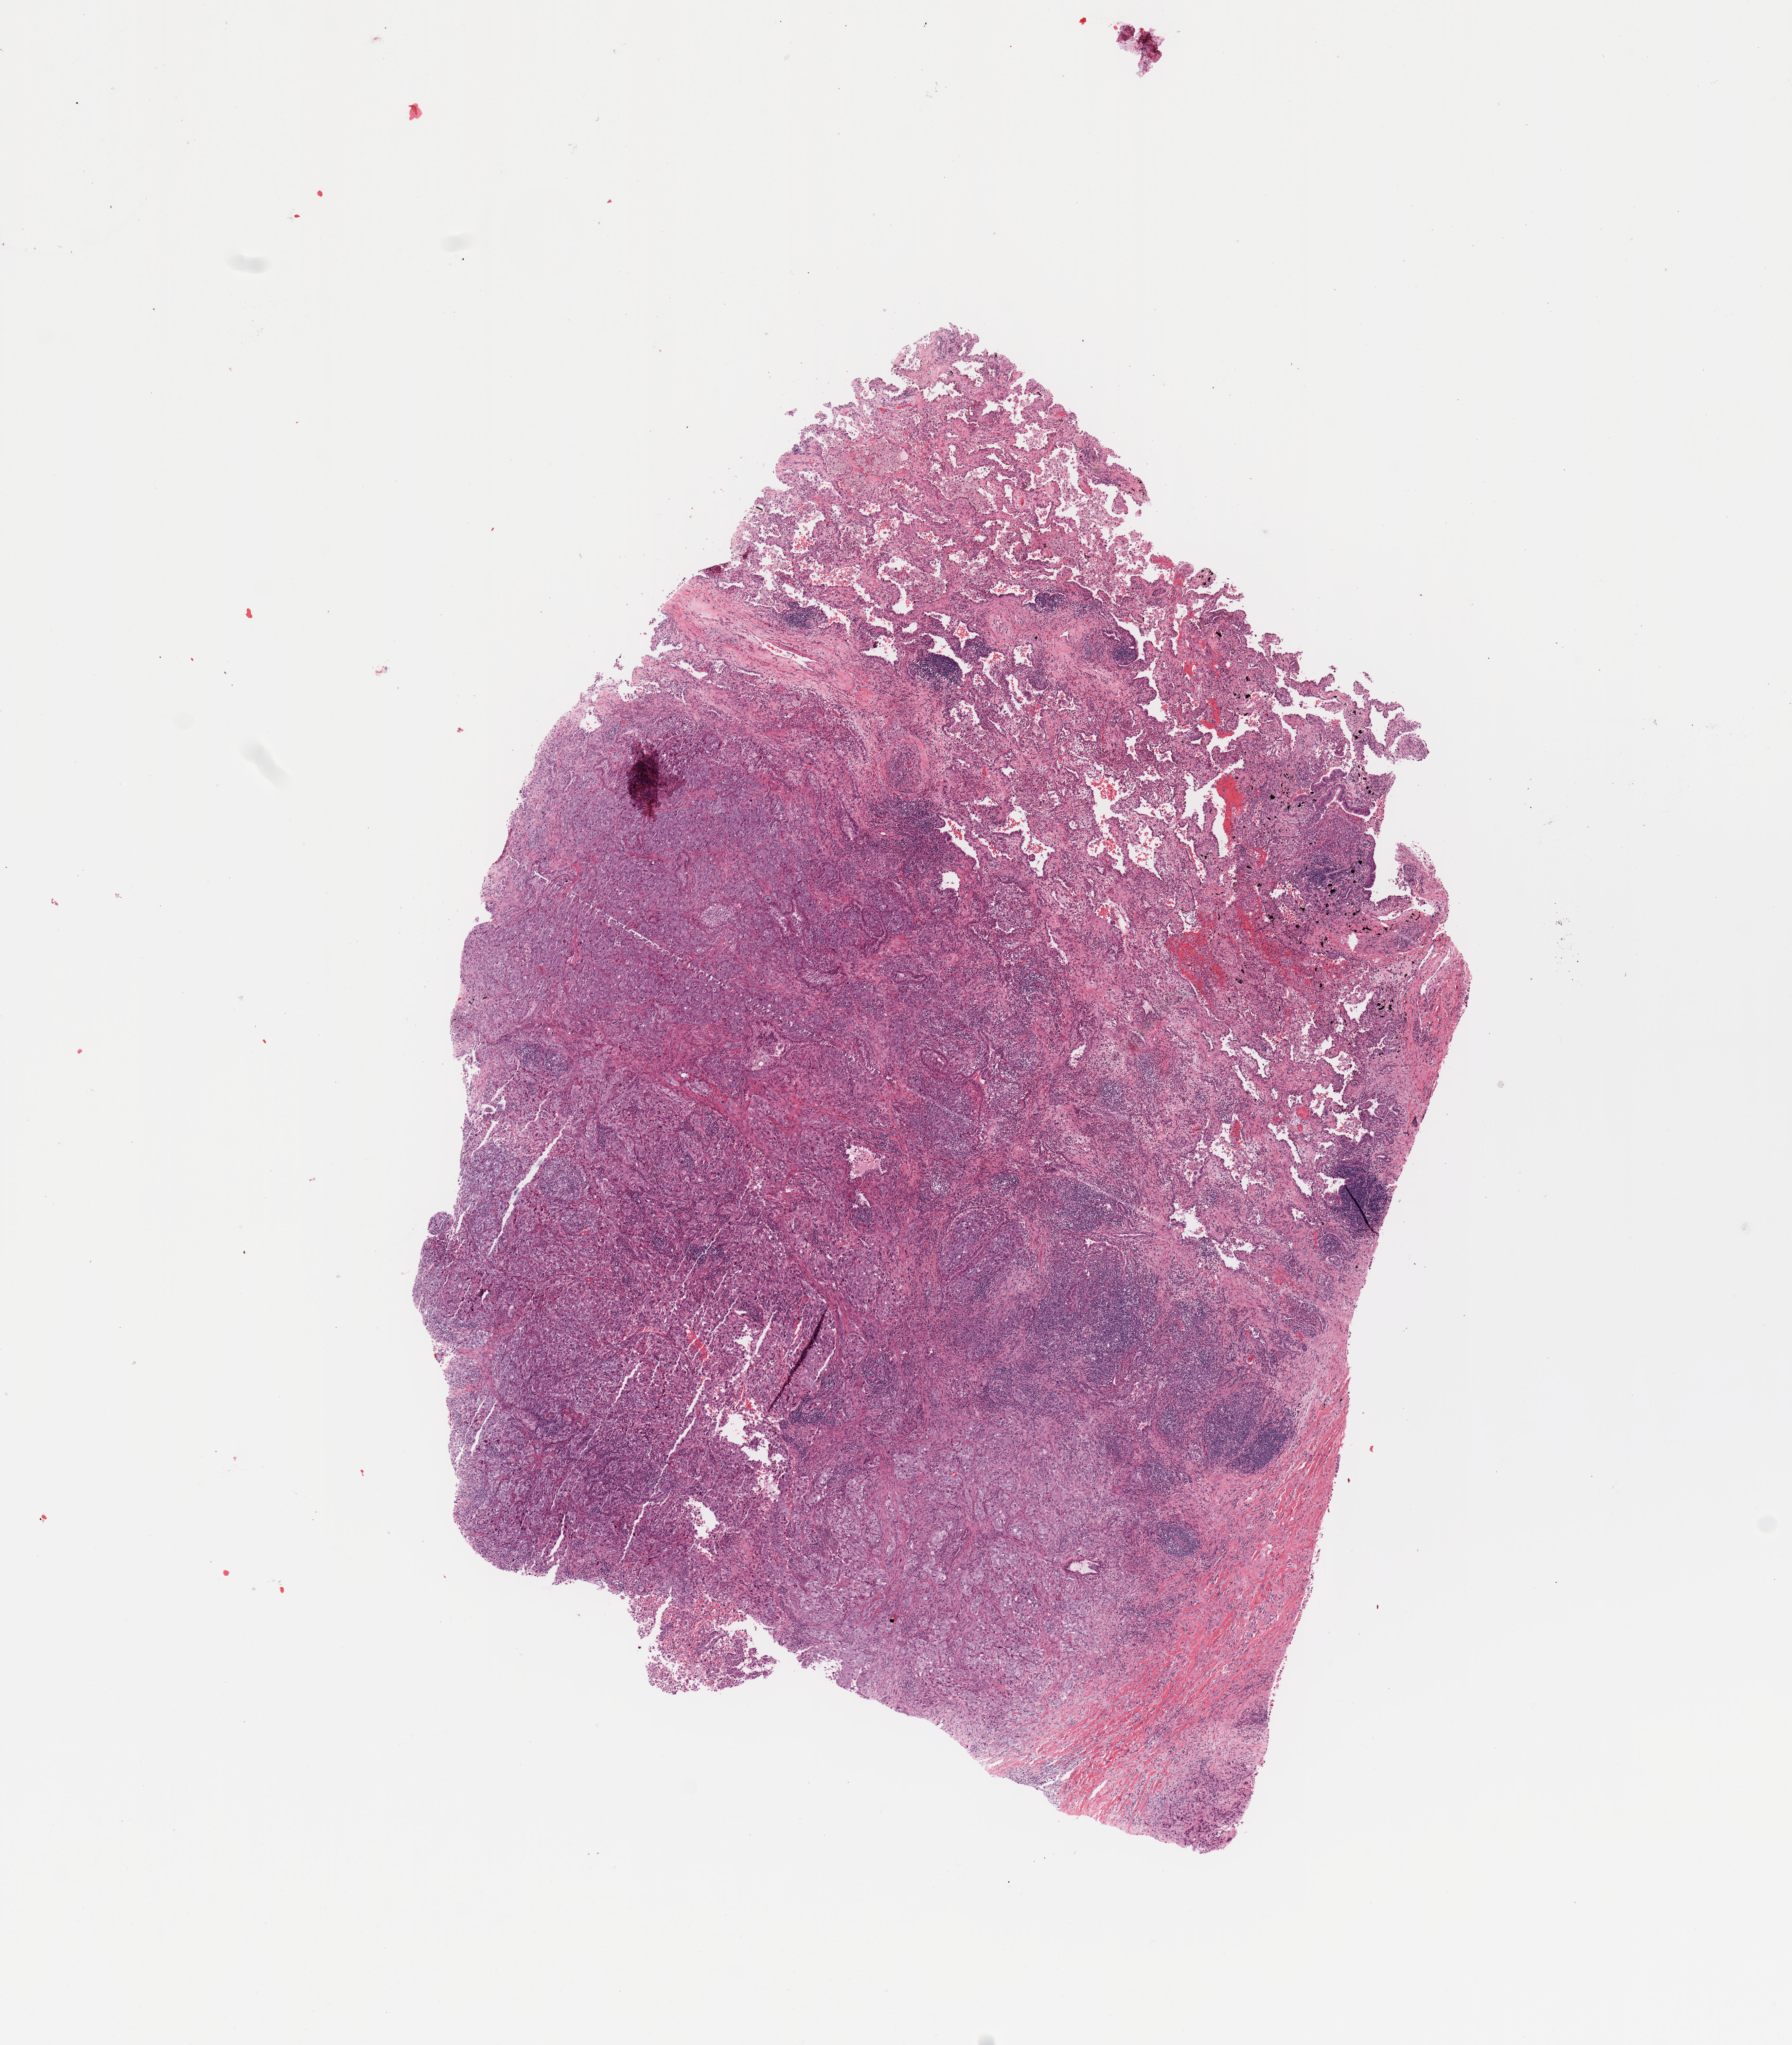
H&E-stained whole-slide image, whole scanned area (about 10.8 x 12.4 mm) shown as a low-resolution overview; tumour tissue sample, sampled site: lung. 62-year-old male patient. Histologic grade: G3 (poorly differentiated). Composition of this section per pathologist review: tumour nuclei 70%, necrosis 5%.
- AJCC pathologic stage: IB
- histologic diagnosis: Adenocarcinoma, NOS